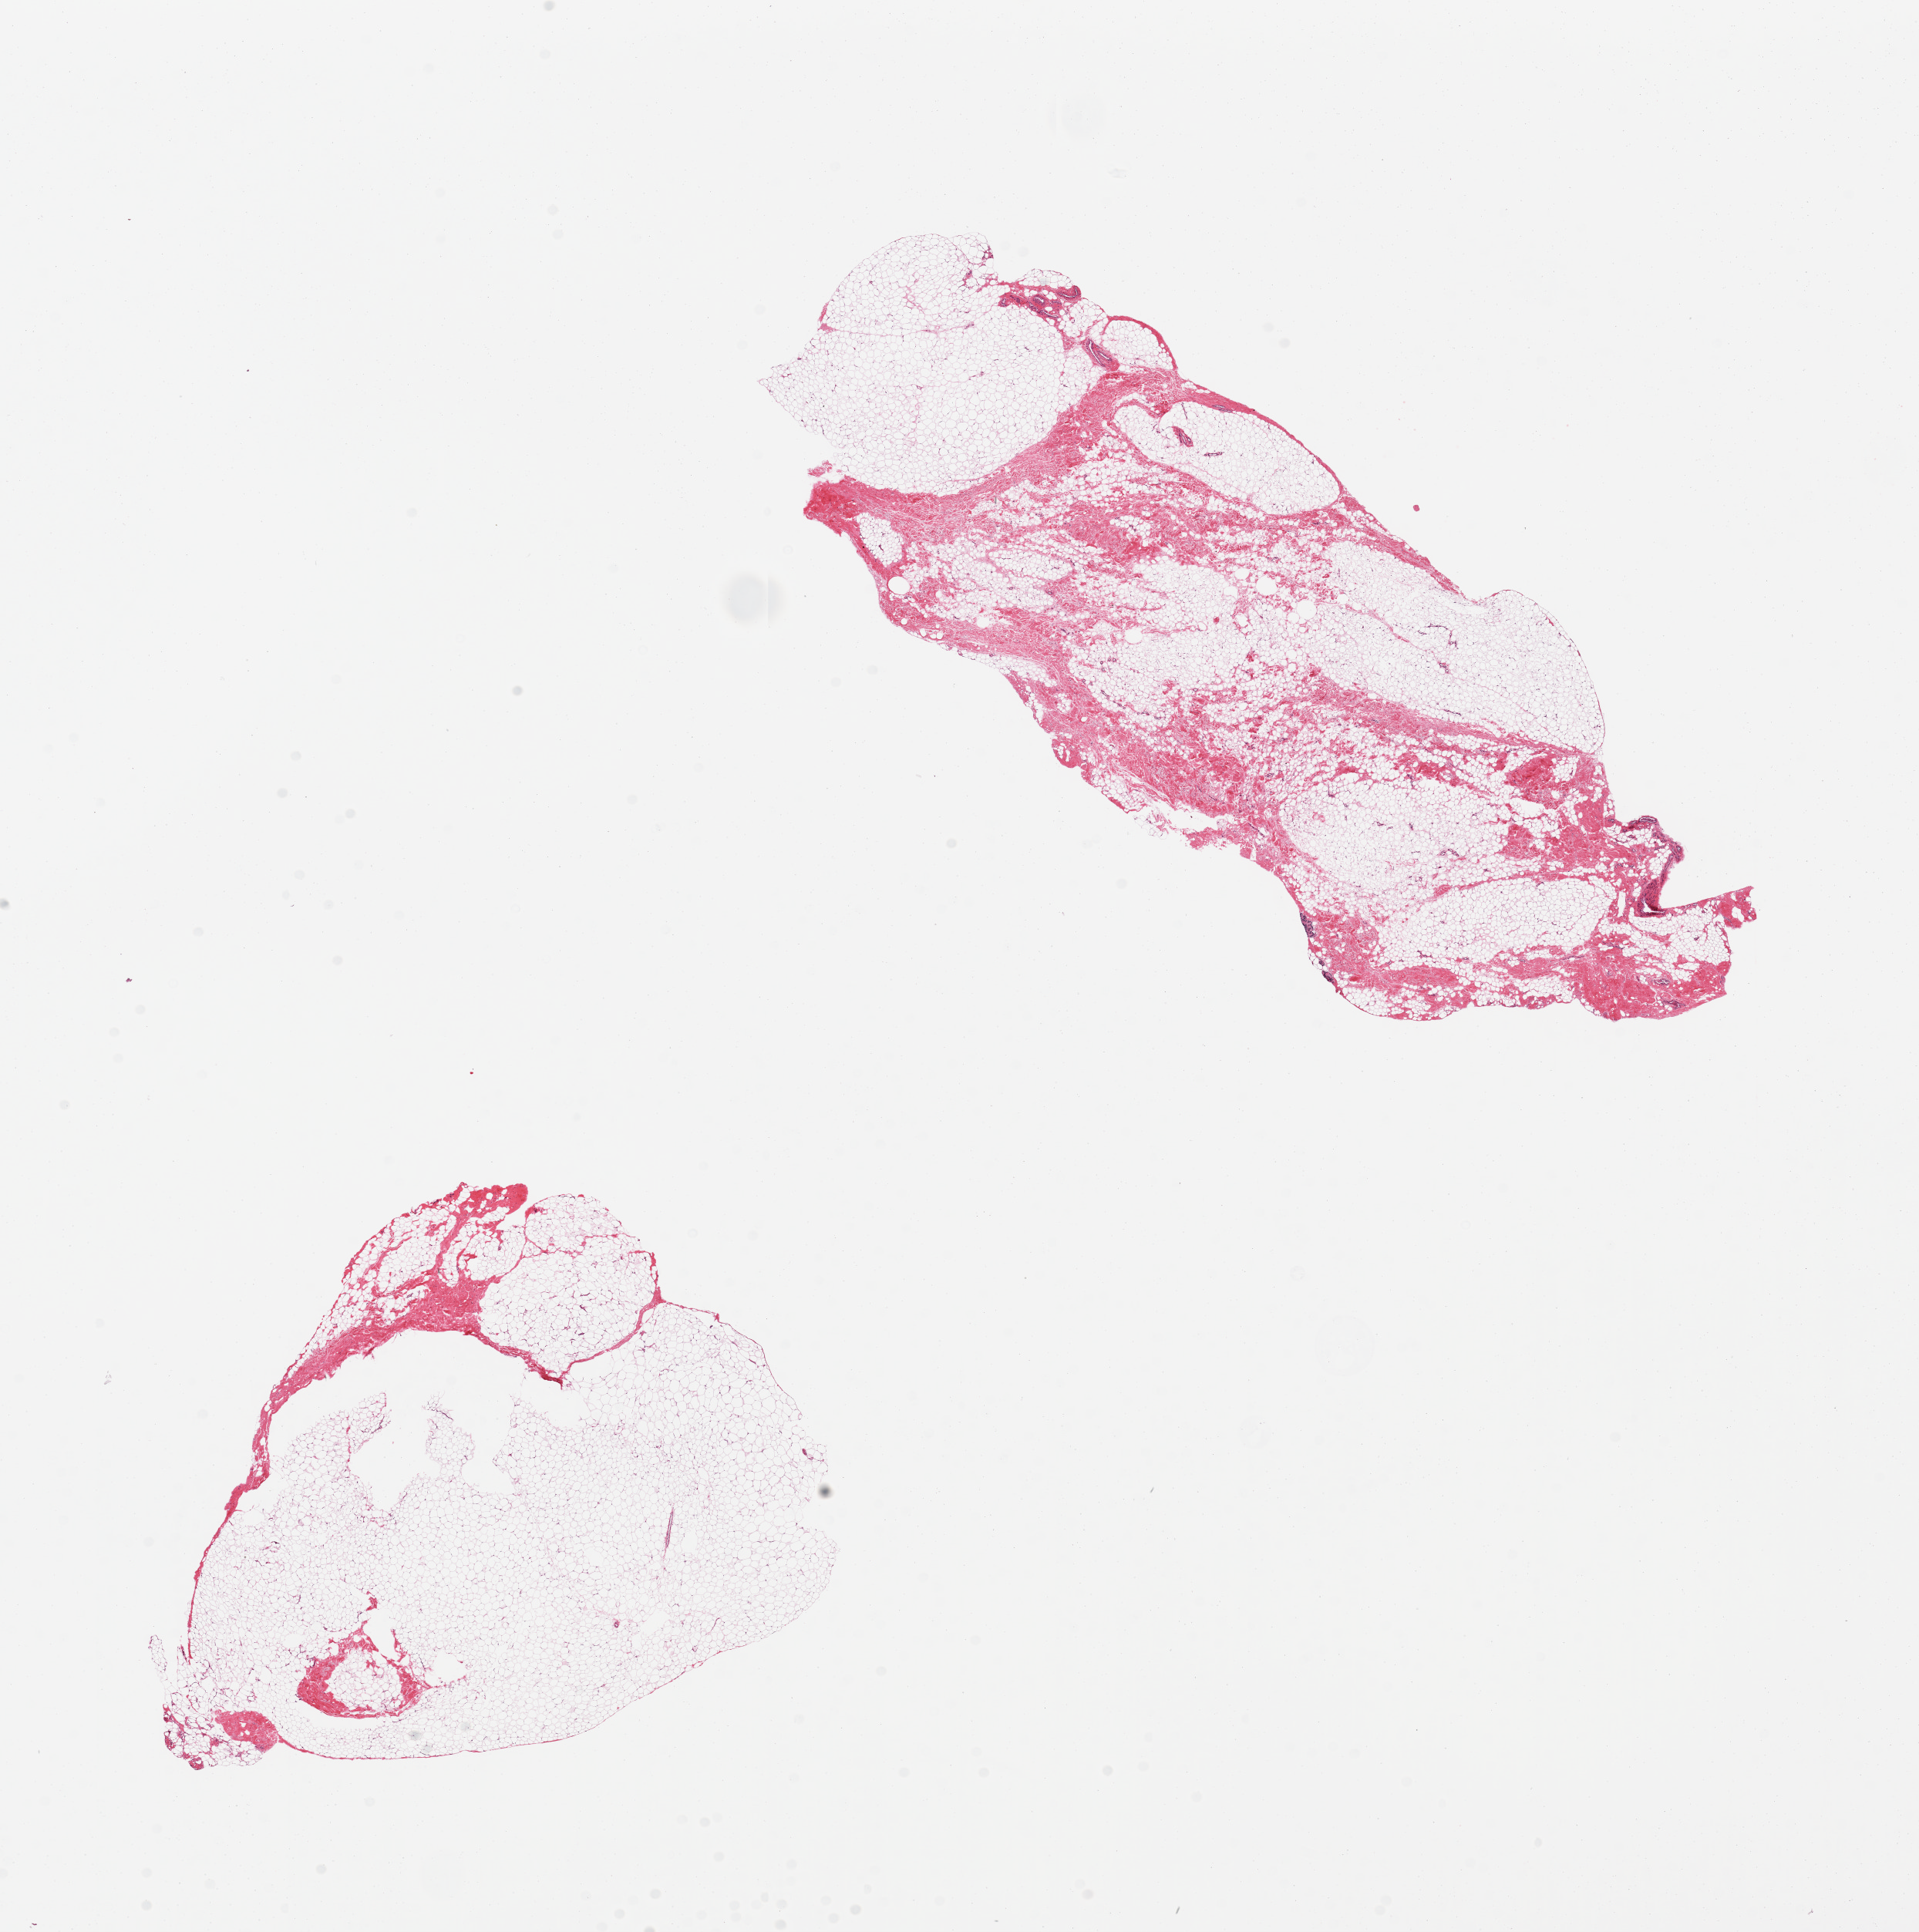
Hematoxylin and eosin (H&E) whole-slide image, brightfield — low-resolution overview of the scanned area, about 19.7 x 19.8 mm (from a 20x scan); PAXgene-fixed, paraffin-embedded tissue; target tissue: breast; tissue donor sample. Donor: male.
Pathologist's review note for this sample: 2 pieces; fibroadipose tissue without ducts.